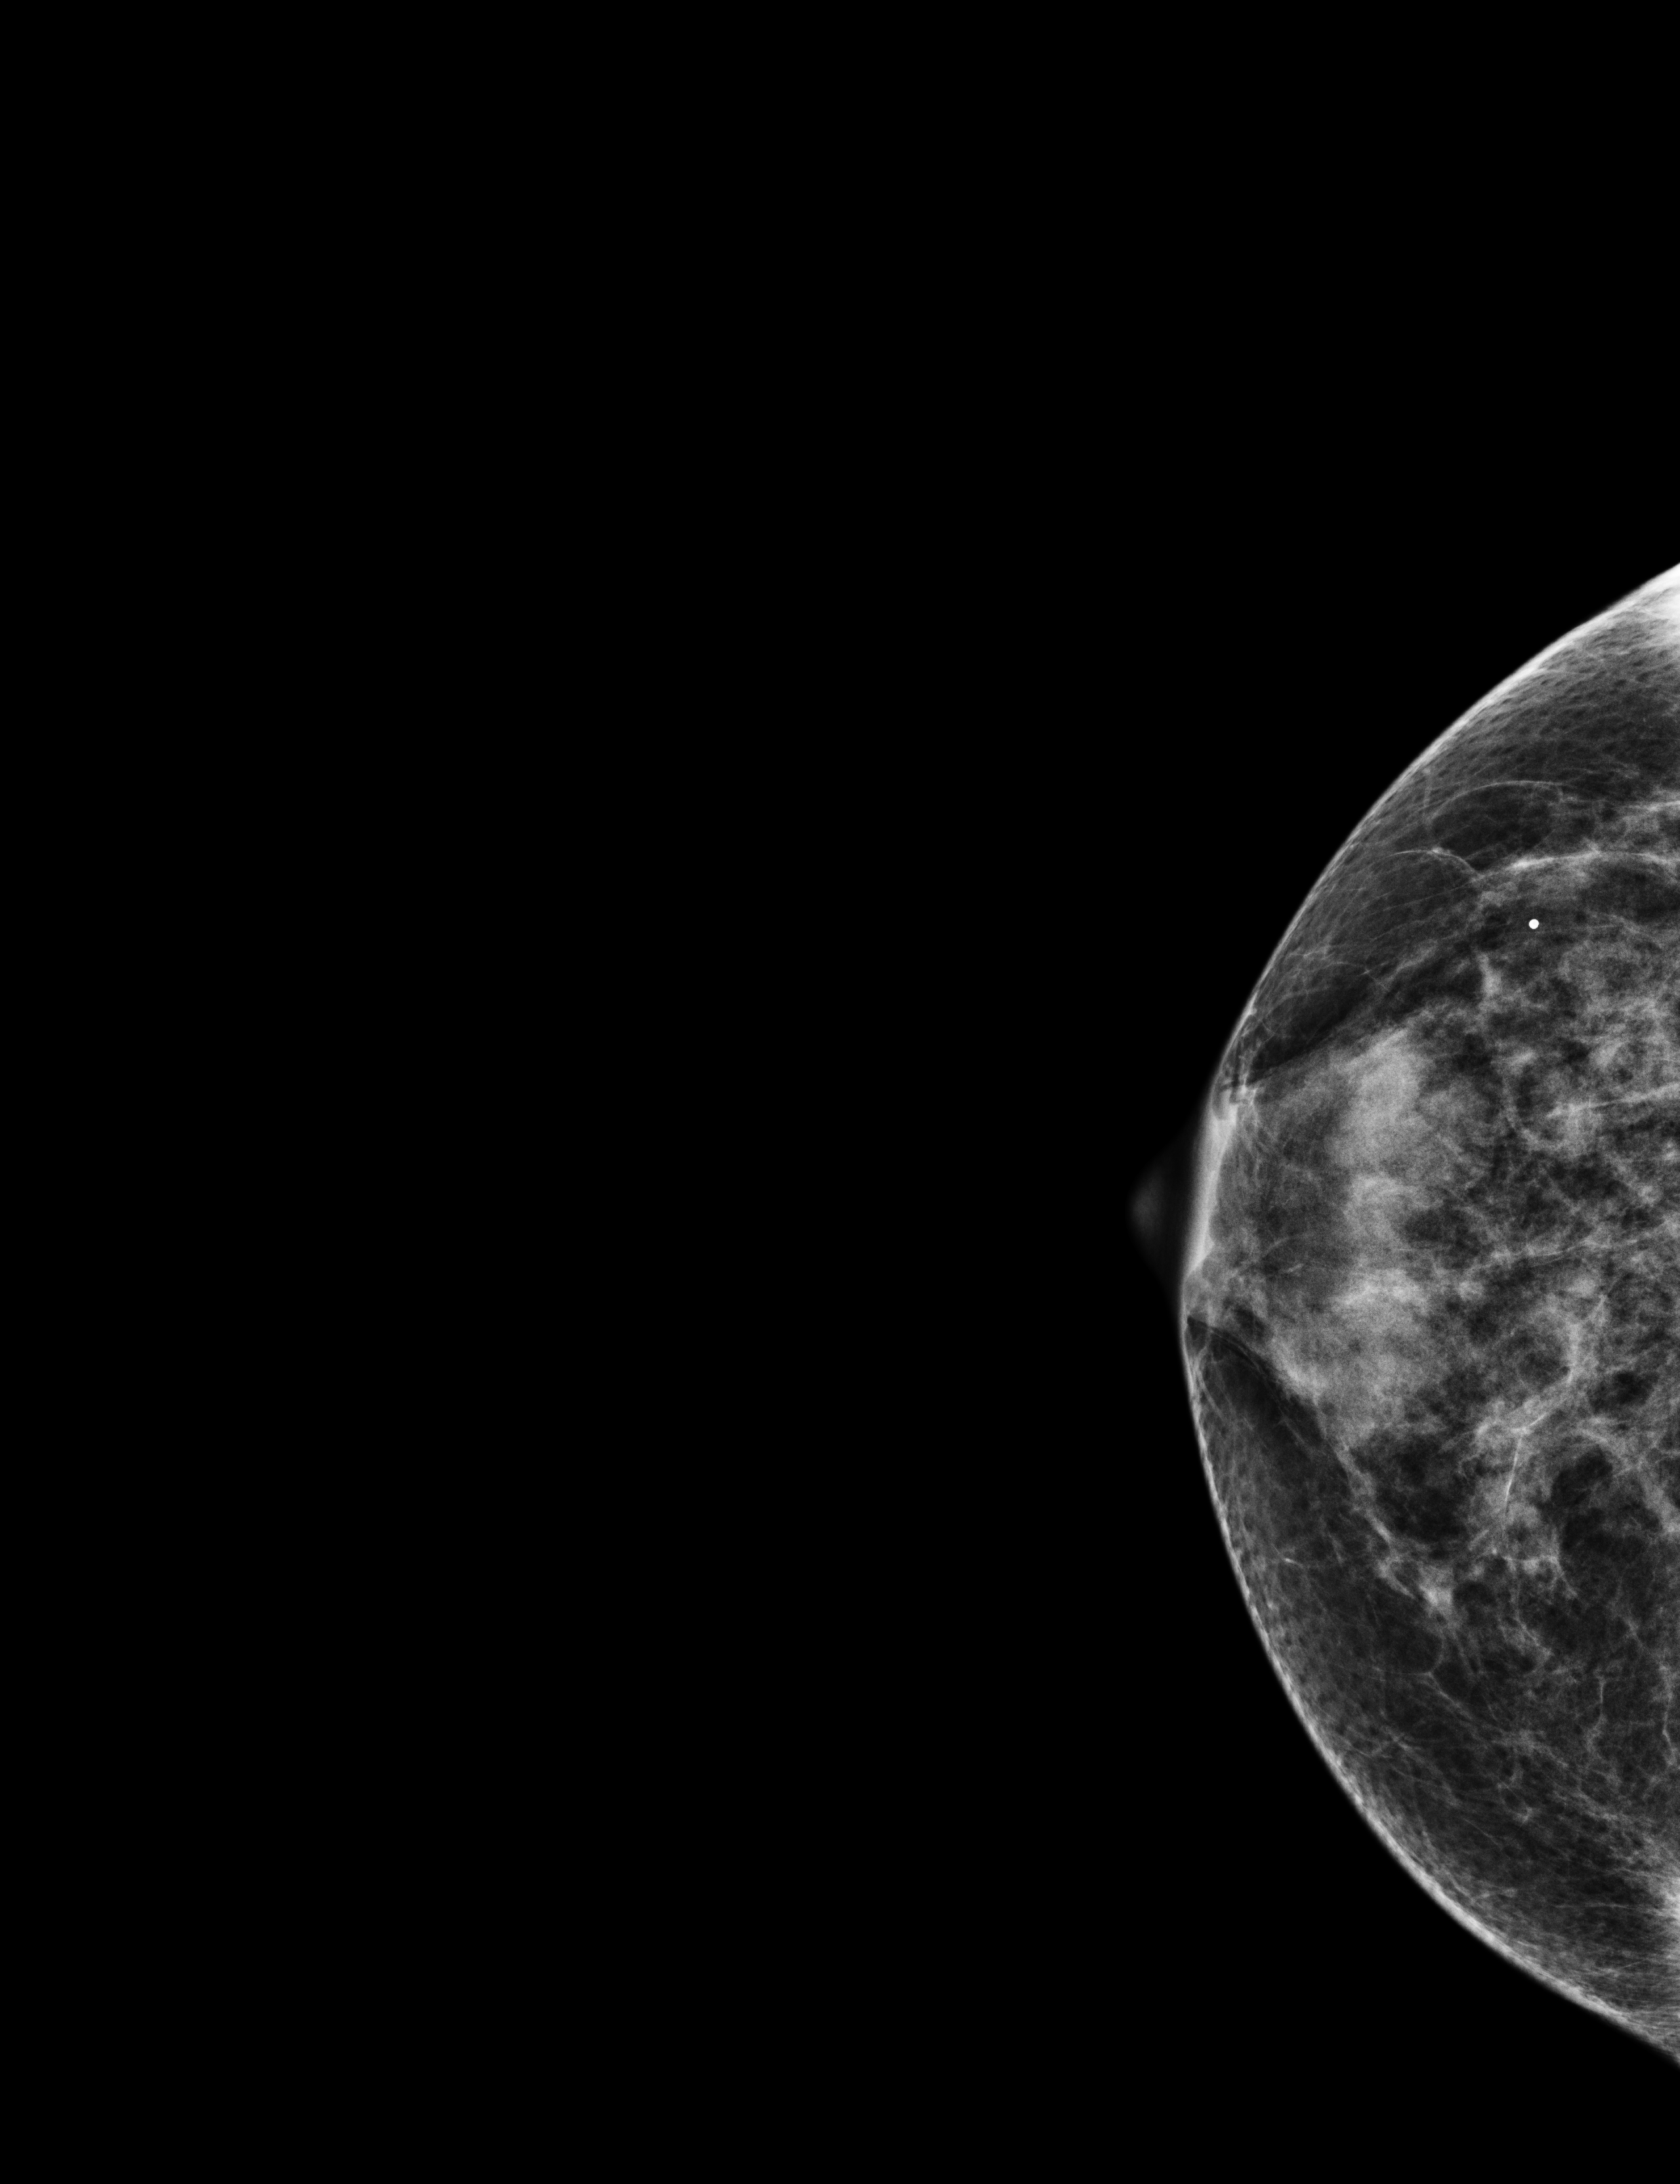
Digital mammogram (FFDM); right breast; craniocaudal (CC) view; screening examination. Female patient, age 59 years.
BI-RADS breast density category at the screening exam (both breasts, scale 1–4): 3. Final BI-RADS category for the screening round (tomosynthesis exam, both breasts): category 1. Recall: no recall after this screen.